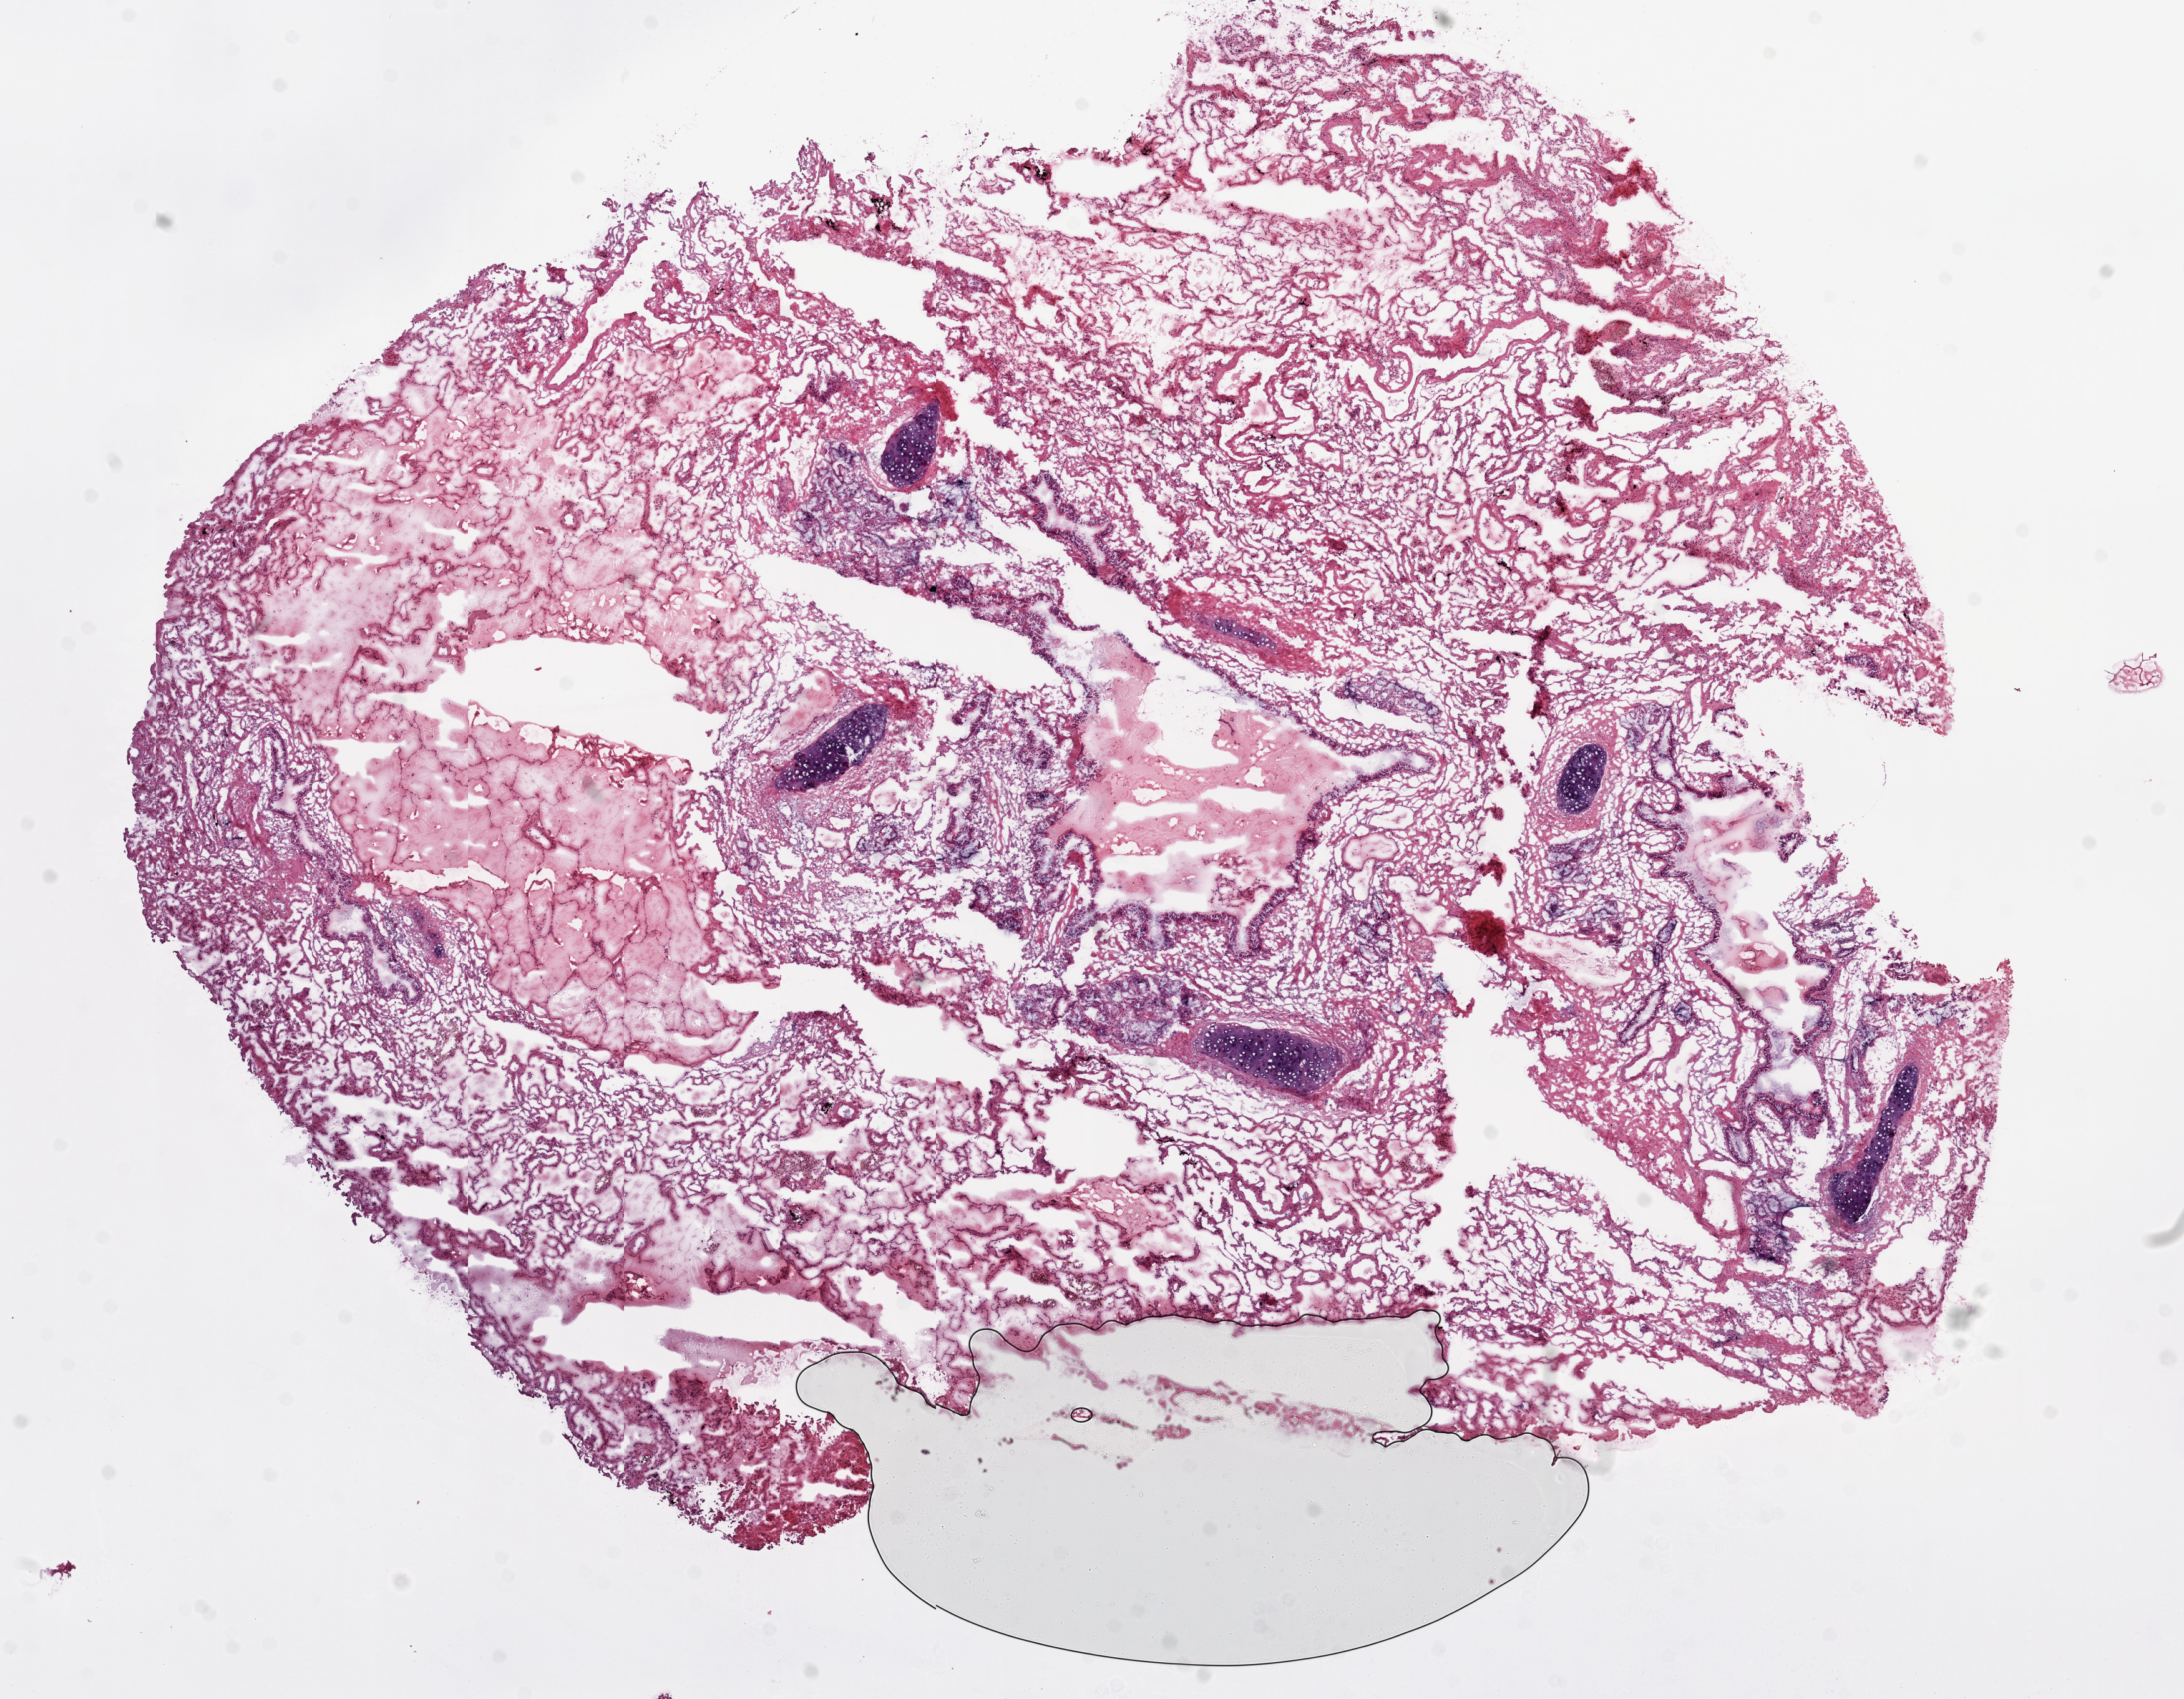
Digitized H&E-stained tissue section (whole slide) — whole scanned area (about 14.0 x 10.9 mm) shown as a low-resolution overview. Frozen section from the top of the tissue portion. Lung, solid tissue normal (non-tumour tissue) sample. Female patient; age at initial diagnosis 72 years.
This section: solid tissue normal (non-tumour) sample from the same patient. Patient diagnosis: Adenocarcinoma, NOS (upper lobe, lung).